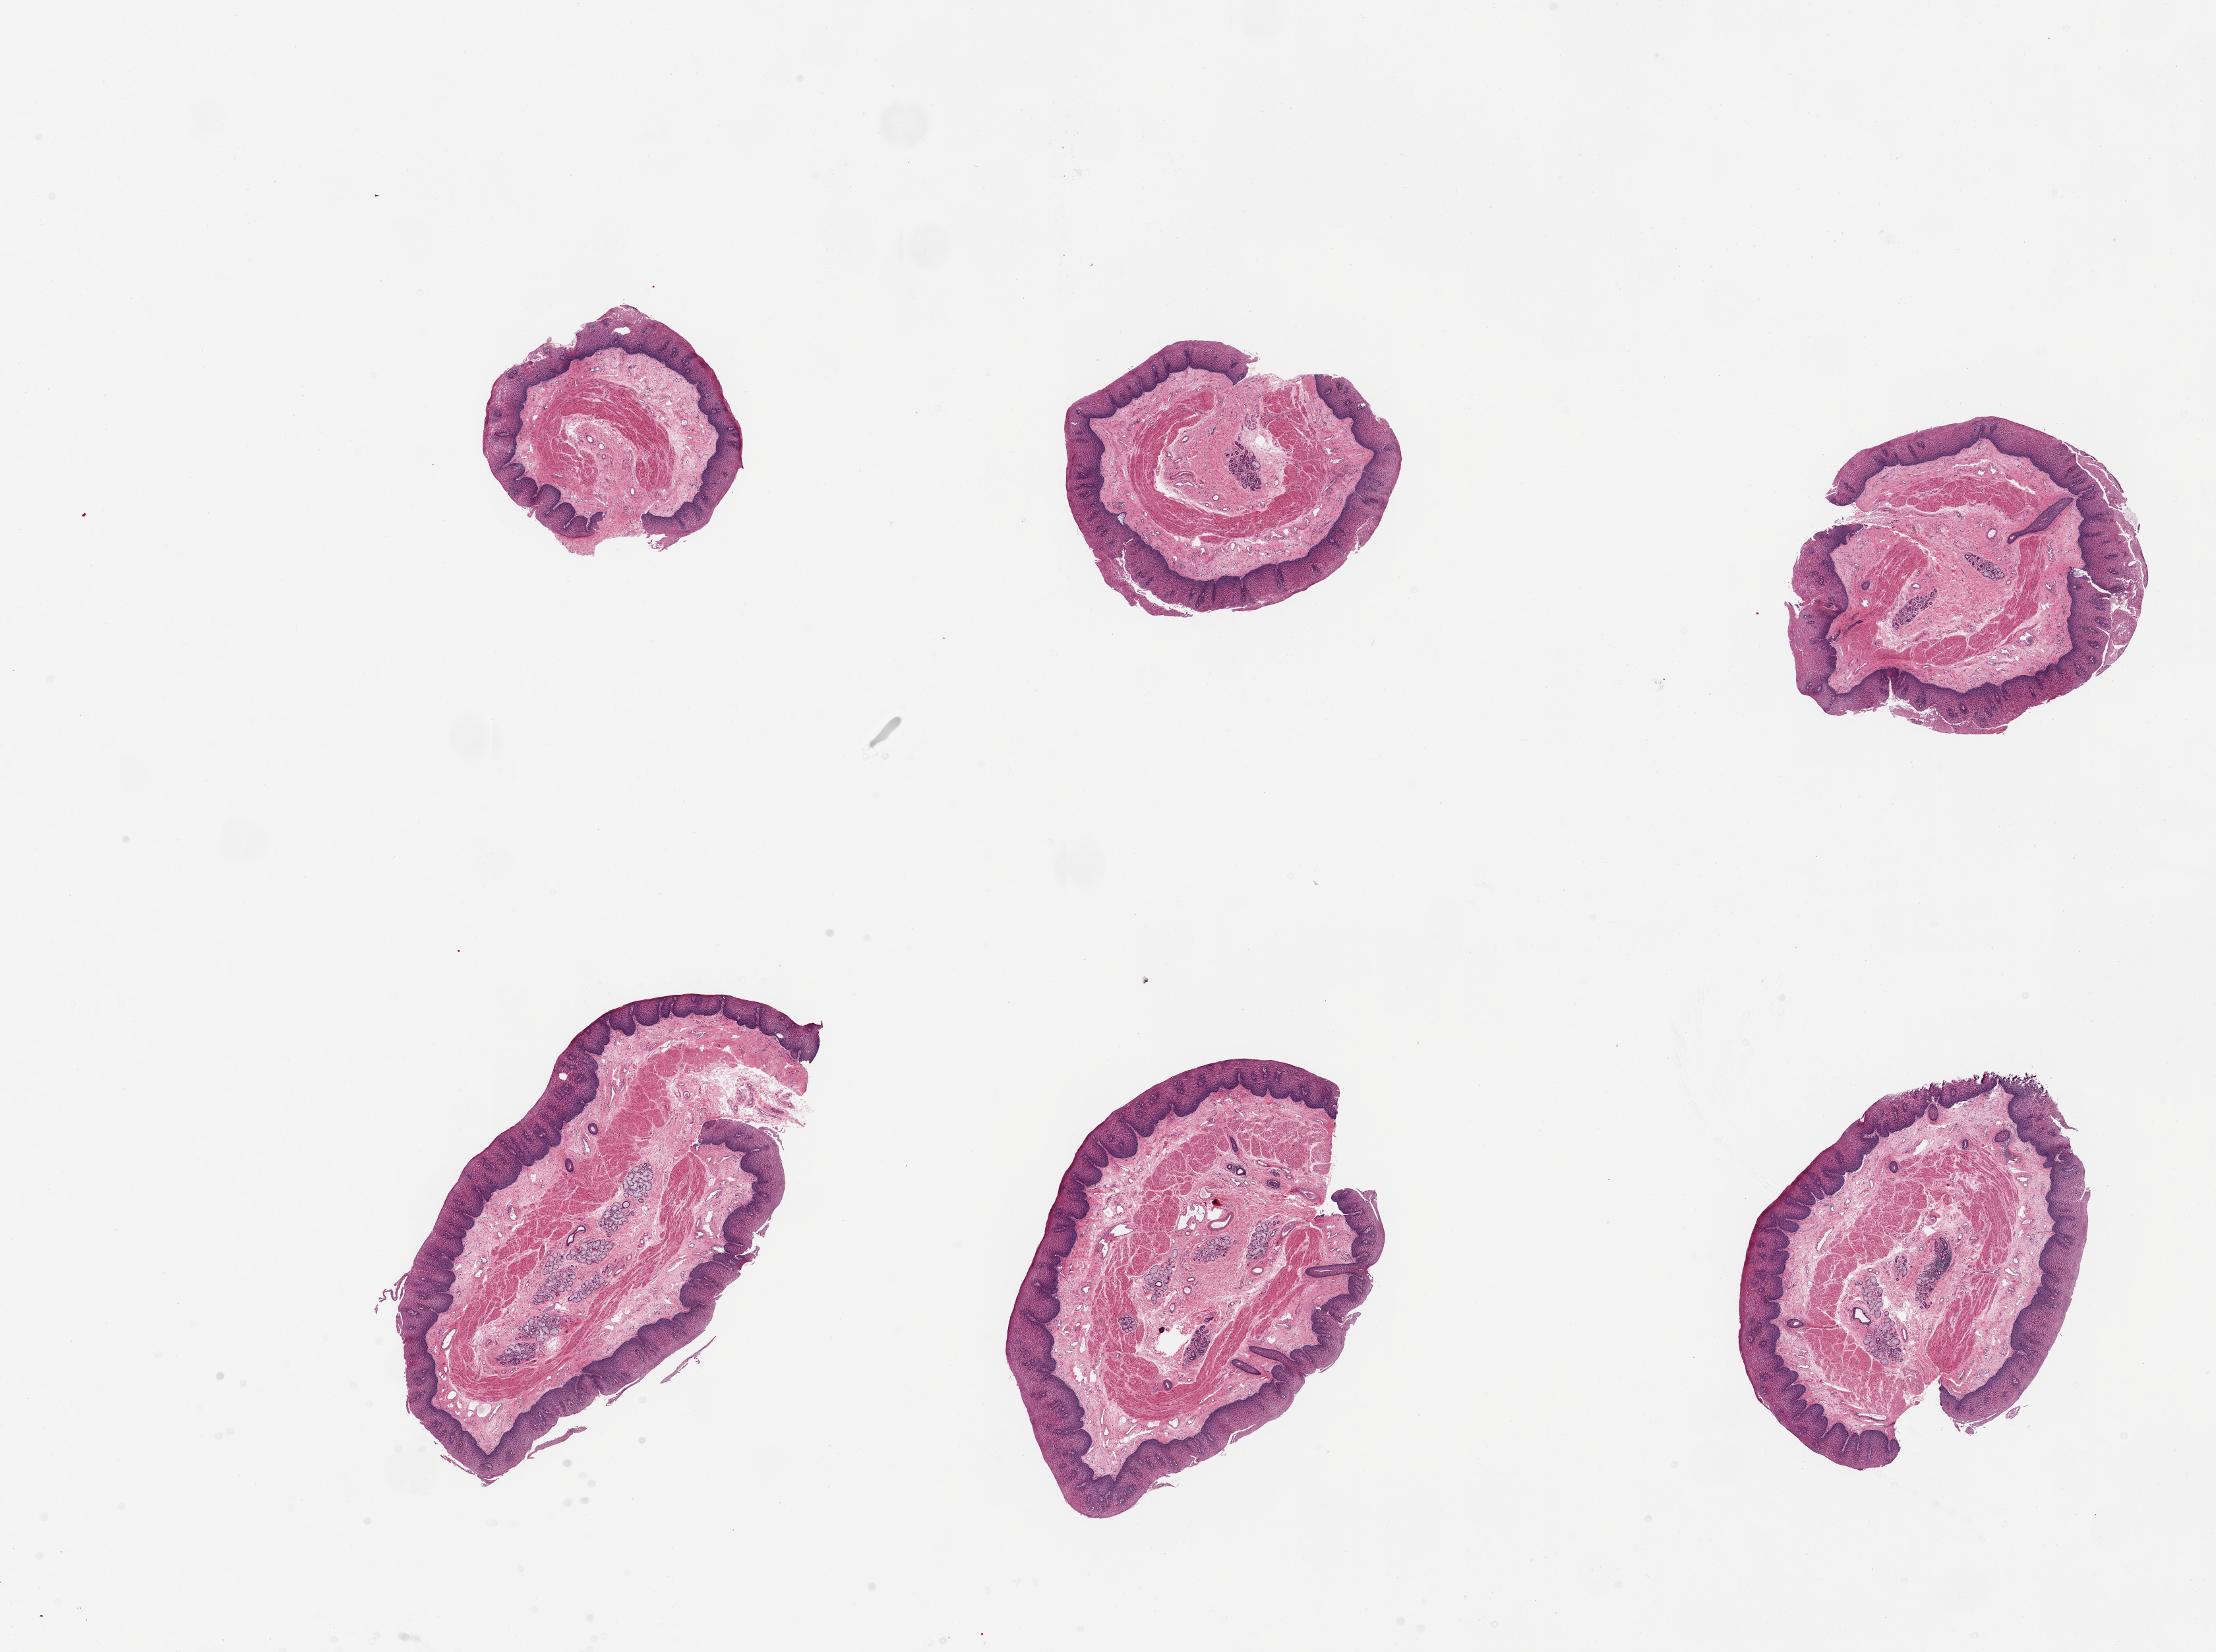
Haematoxylin and eosin whole-slide image, brightfield — a low-resolution overview of the entire scanned area, about 26.6 x 19.8 mm. PAXgene-fixed paraffin-embedded (PFPE) section. Sampled site (target tissue): esophageal mucous membrane. Donor tissue sample. Donor sex: male.
Pathologist's review note for this sample: 6 pieces, squamous mucosa up to ~0.5mm, ~20% thickness; Numerous submucosal mucus glands present.